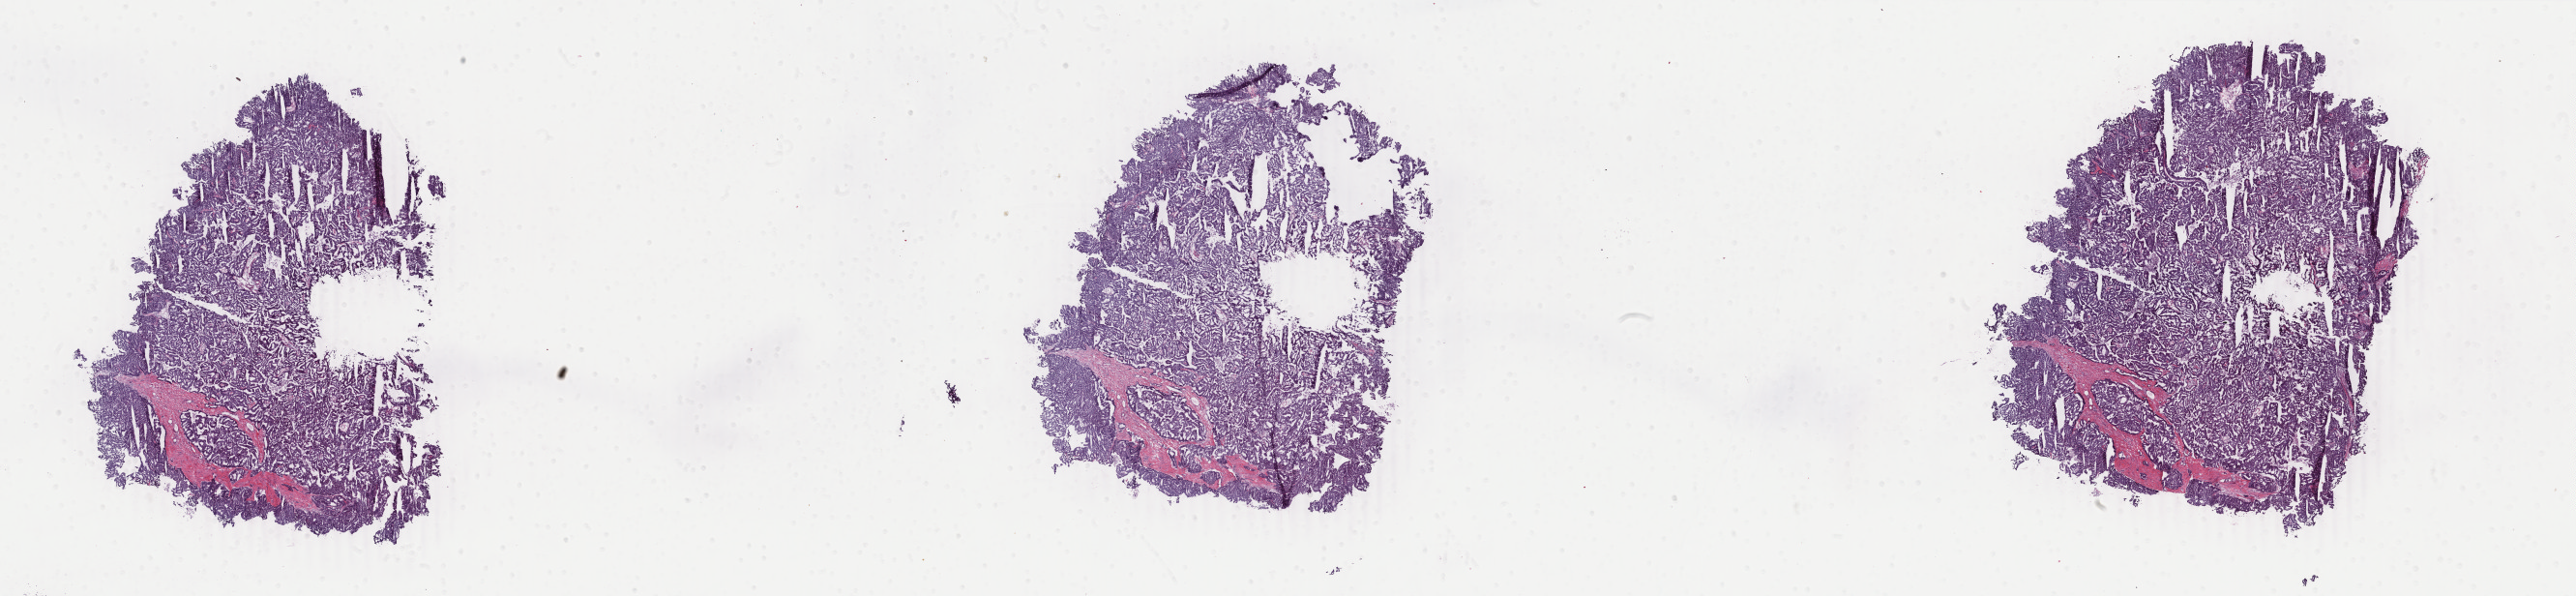
Digitized H&E tissue section (whole slide), a low-resolution overview of the entire scanned area, about 42.4 x 9.8 mm; frozen section; breast, primary tumour sample. Female patient. Pathologist review of this section (percent, as recorded): tumour cells 95%, tumour nuclei 95%, normal cells 0%, stromal cells 5%, necrosis 0%. Inflammatory infiltration, as recorded: lymphocyte infiltration 0%, monocyte infiltration 0%, neutrophil infiltration 0%.
* histologic diagnosis: Intraductal papillary adenocarcinoma with invasion